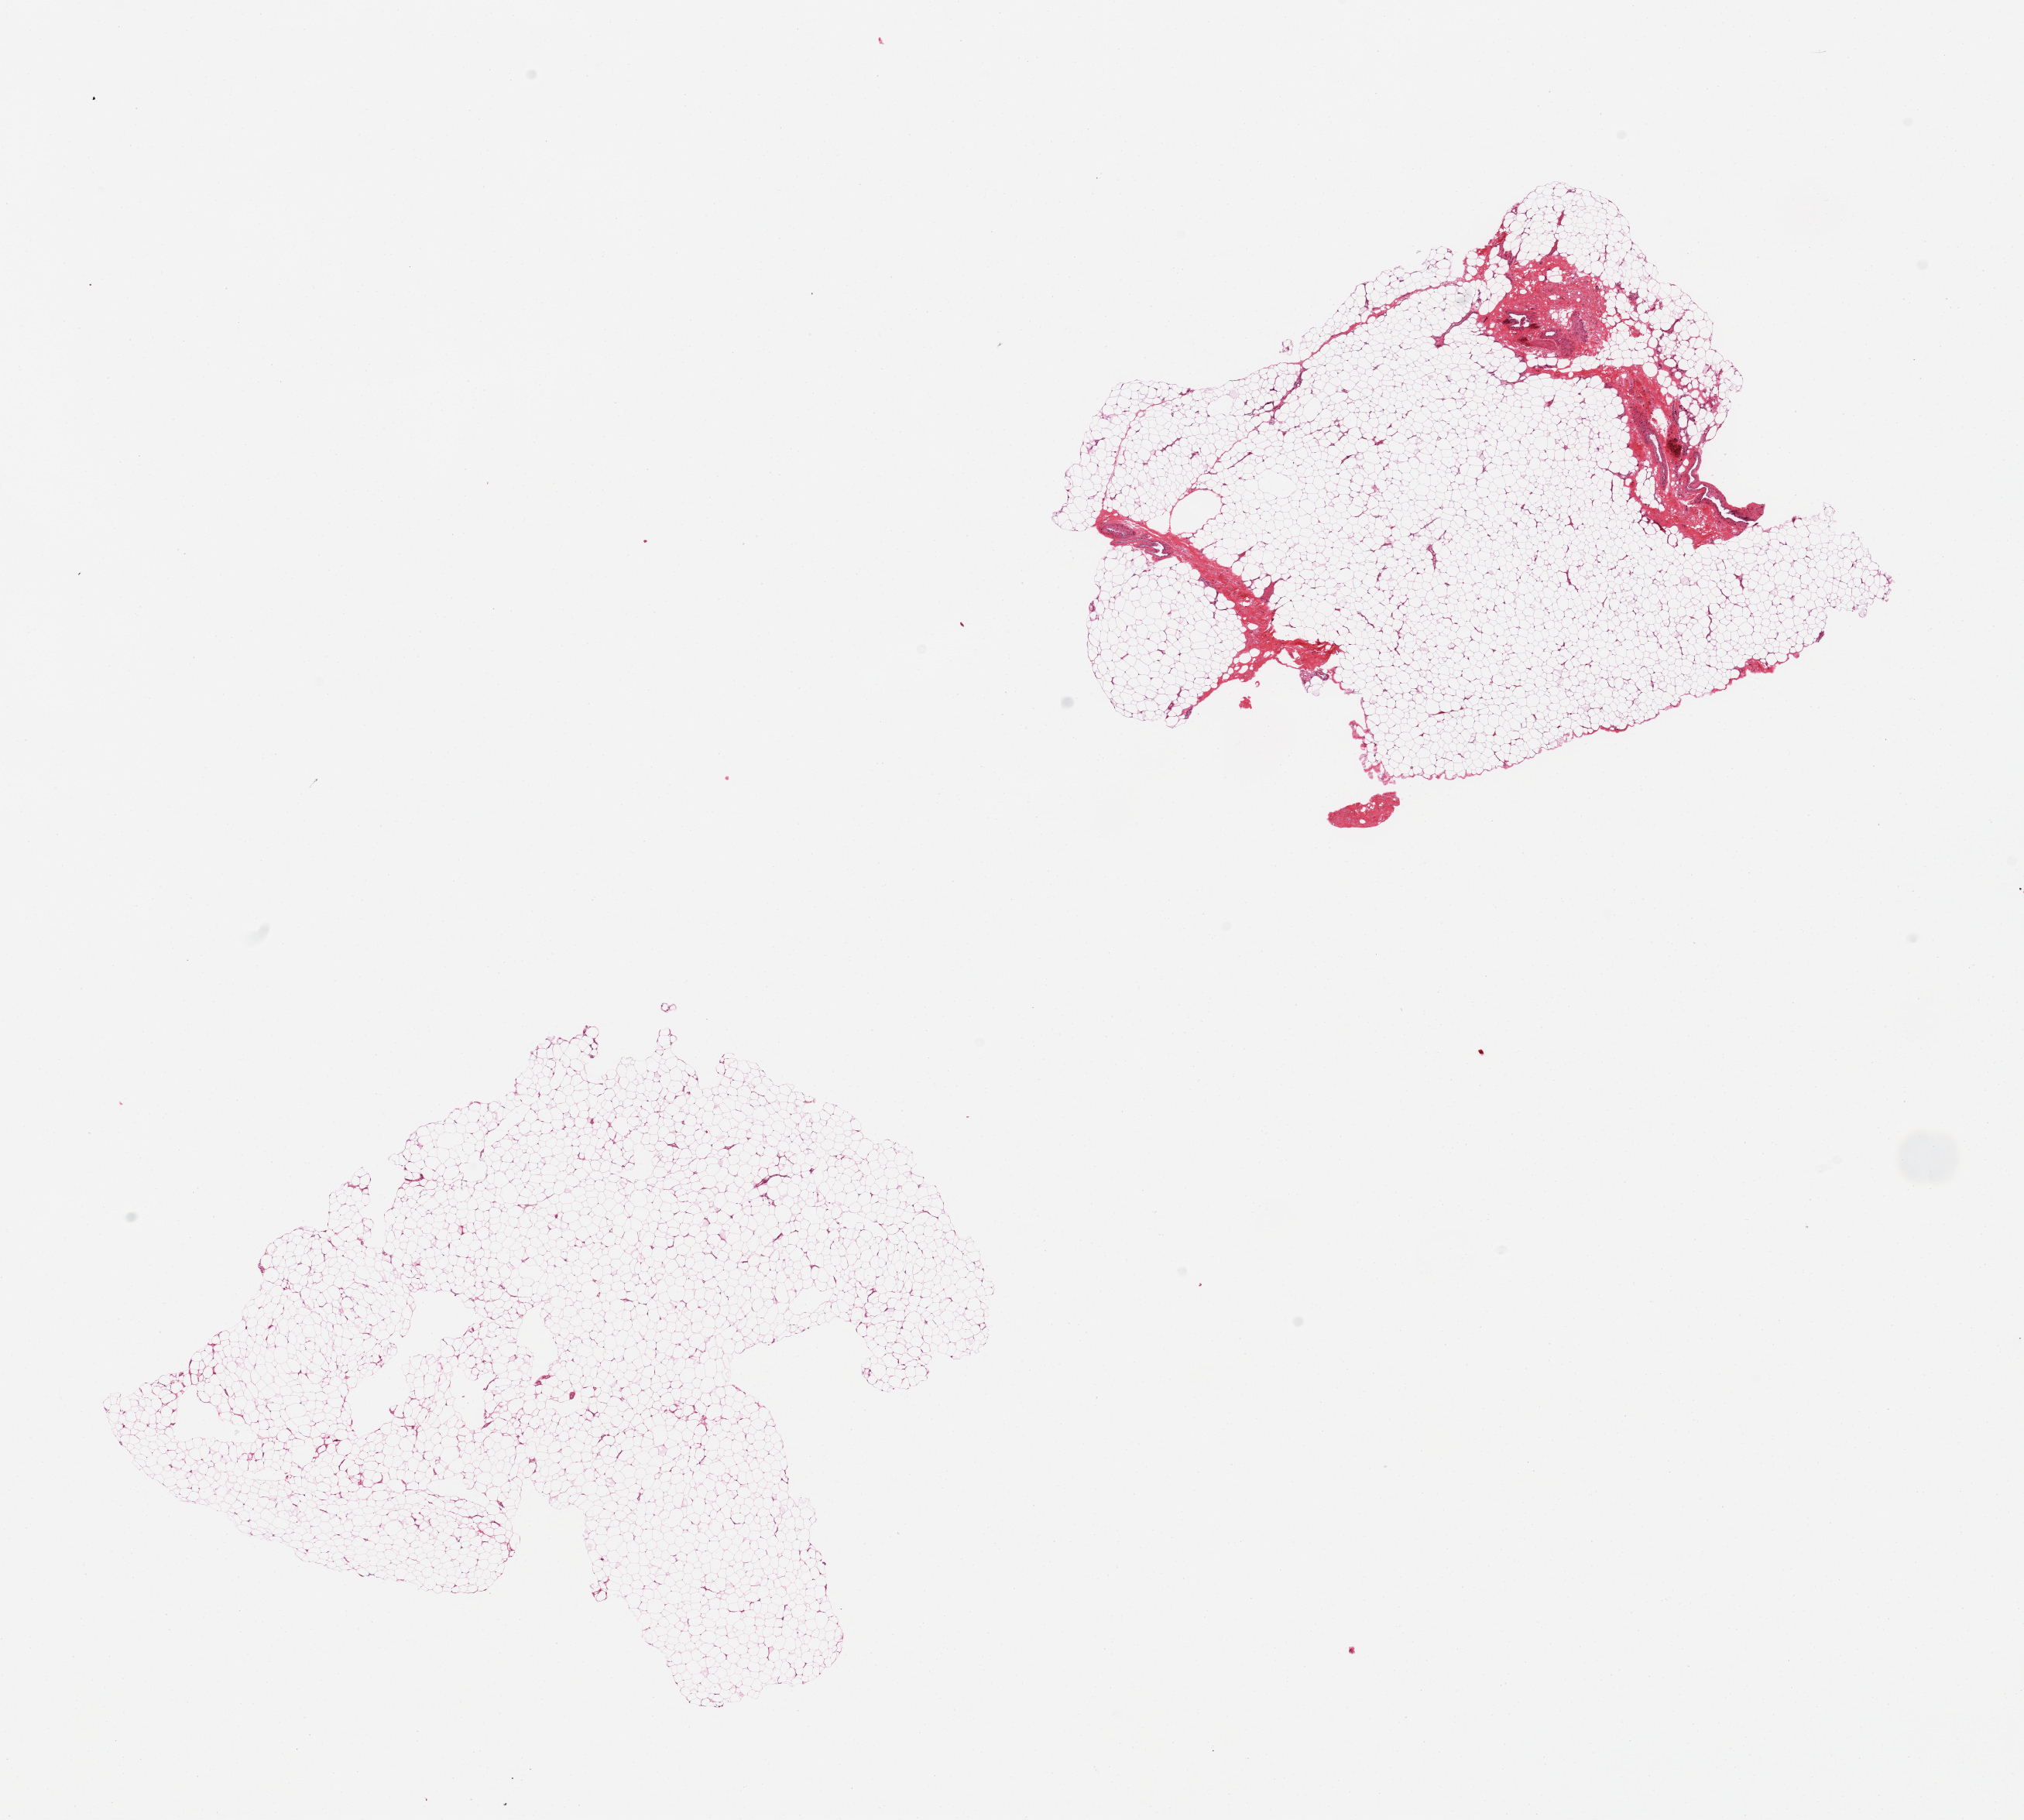
Whole-slide image, hematoxylin and eosin (H&E) stain, whole scanned area (about 20.7 x 18.6 mm) shown as a low-resolution overview; PAXgene-fixed, paraffin-embedded tissue; section of adipose tissue (target tissue); donor tissue sample. Donor: female.
Reviewer comment on this tissue sample: 2 pieces, ~10% fibrovascular elements.